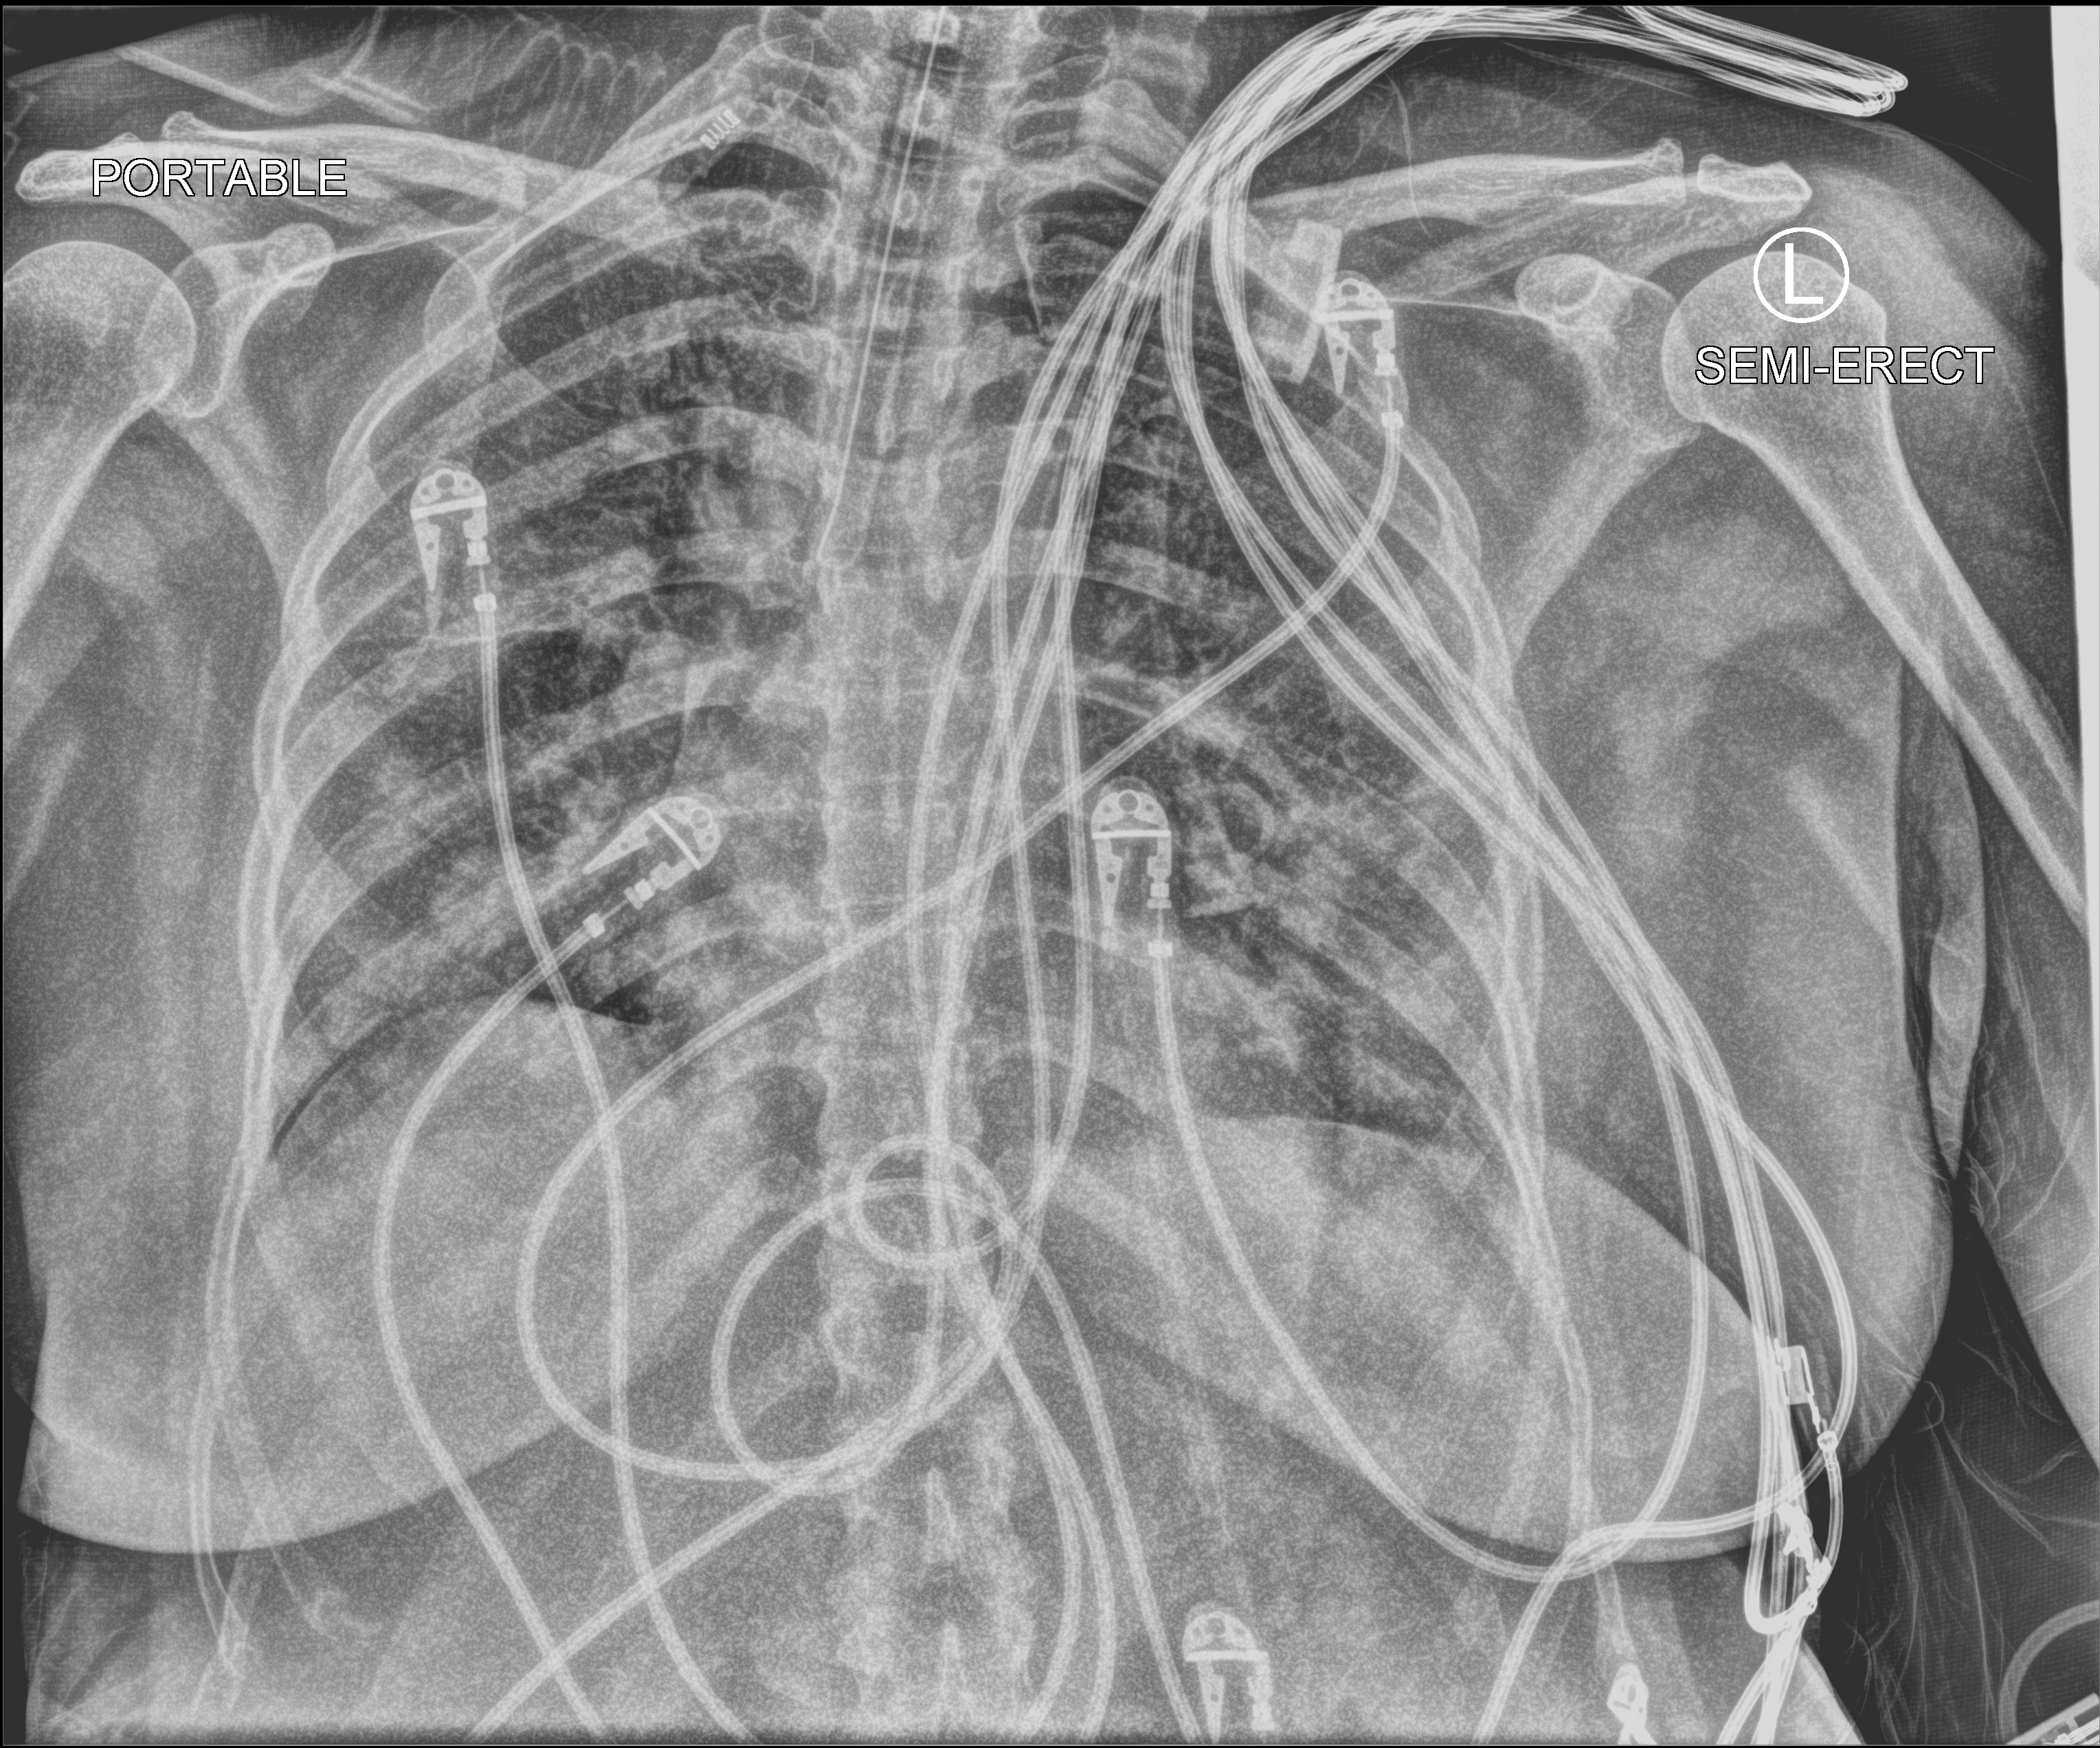
Portable chest radiograph, anteroposterior (AP) projection. Male patient hospitalised with COVID-19, age 18–59 years.
Admission-level facts for this patient (not findings on this image; timing relative to this image not recorded): mechanically ventilated during this hospital stay: yes.